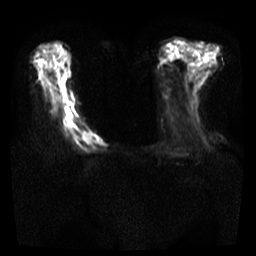
Breast MRI, one axial slice; diffusion-weighted series; image 2 of 4 stored at this slice position (different b-values; order by instance number); 3 T; 5 mm slice thickness; 256 × 256 image matrix, field of view 300 × 300 mm. Female patient.
Structures marked on this image (expert manual segmentation):
- tumour on diffusion-weighted imaging: bounding box <78,129,105,148> (left, top, right, bottom; pixels)